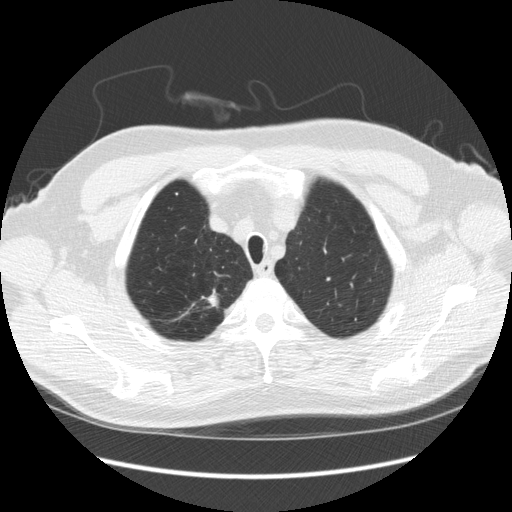
Axial slice from a low-dose chest CT screening exam. Third annual screen. Lung window (W 1500 / L -600 HU). 2.5 mm slice thickness. Slice 30 of 248 in the series. 512 × 512 image matrix. Male, age 64 years at enrolment. Former smoker at enrolment.
- Lesion marked by an expert reader, bounding box [x1, y1, x2, y2] px = [187, 285, 229, 321].
- The screening reader recorded 4 non-calcified nodules or masses ≥4 mm on this exam; which of them this box marks is not recorded.
- Participant outcome: lung cancer diagnosed 15 days after this screen — adenocarcinoma, NOS, right upper lobe, moderately differentiated (G2), stage IA (AJCC 6th edition), 14 mm at pathology.